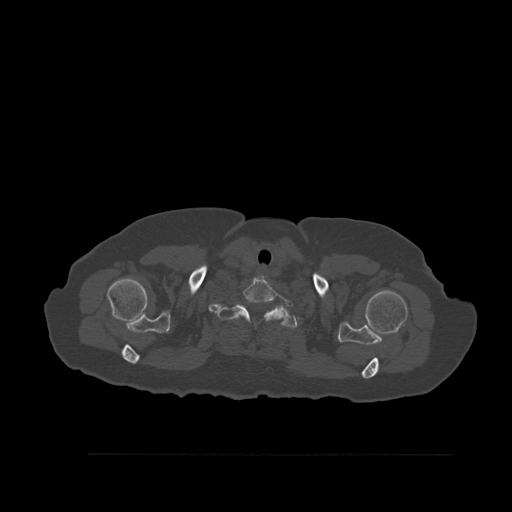
CT including the spine, one axial slice. Position 448 of 527 along the scan axis. Bone window (W 1800 / L 400 HU). 512 × 512 image matrix, field of view 470 × 470 mm. Patient: female, 73 years. From the clinical record (not read from this slice): primary cancer: breast; vertebrae with lytic lesions (as recorded): L2.
Annotated regions visible in this slice (semi-automatic segmentation, software-assisted and operator-edited):
- T1 vertebra: box from (x=216, y=305) to (x=298, y=330) px